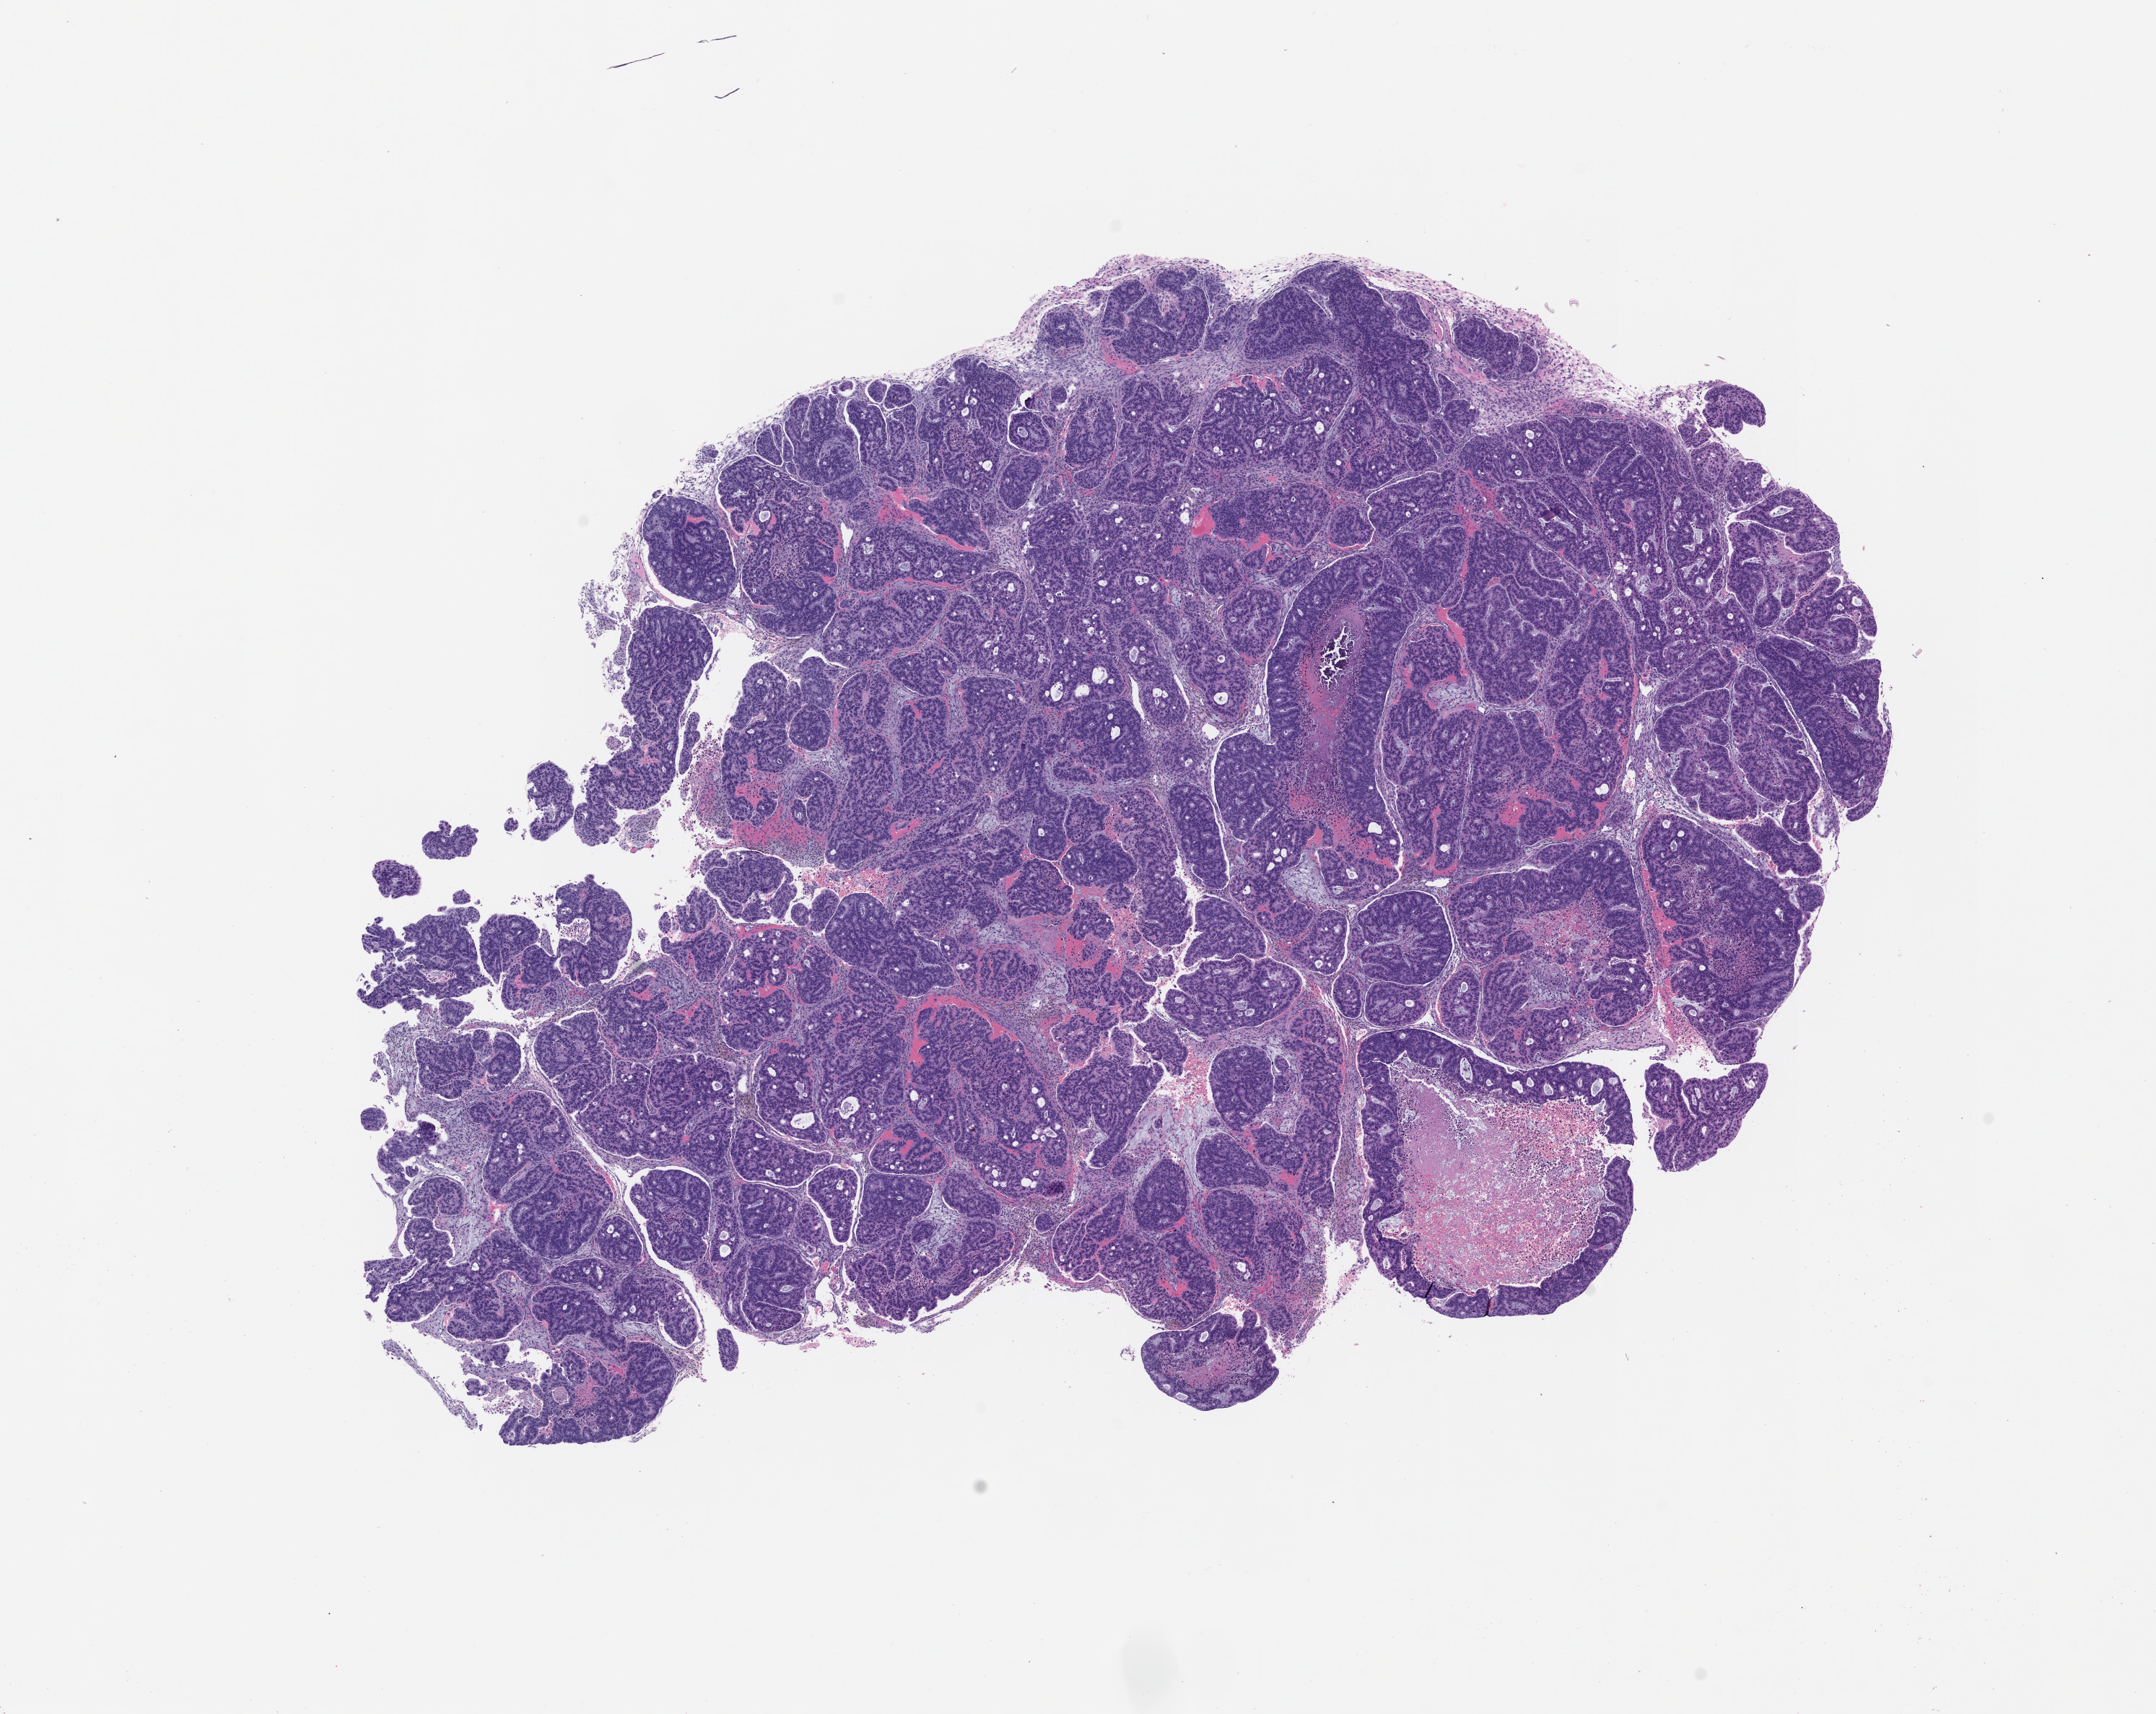
Whole-slide image, hematoxylin and eosin (H&E): patient-derived xenograft (human tumor grown in a mouse), passage 1, low-resolution overview of the scanned area, about 12.0 x 9.5 mm. FFPE section. Originating tumor site category: colon.
- originating patient diagnosis: Colon Adenocarcinoma